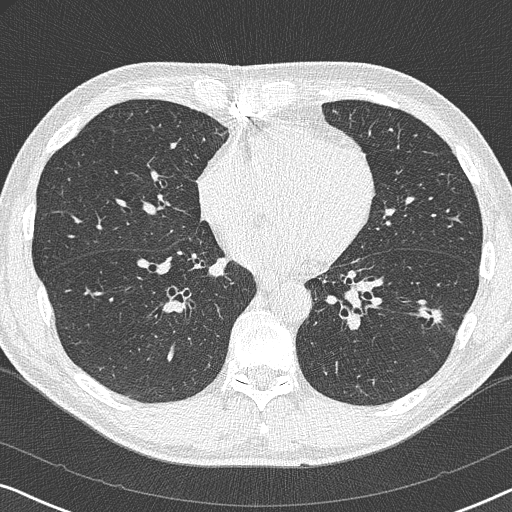
Axial slice from a low-dose chest CT screening exam; first (baseline) screen; lung window (W 1500 / L -600 HU); 1 mm slice thickness; lung (sharp) reconstruction kernel (B50f); 120 kVp; 512 × 512 image matrix, field of view 330 × 330 mm. Male, age 59 years at enrolment. Current smoker at enrolment.
Lesion marked by an expert reader, bounding box [x1, y1, x2, y2] px = [415, 302, 452, 342]. The screening reader recorded 2 non-calcified nodules or masses ≥4 mm on this exam (left lower lobe, right middle lobe); which of them this box marks is not recorded.